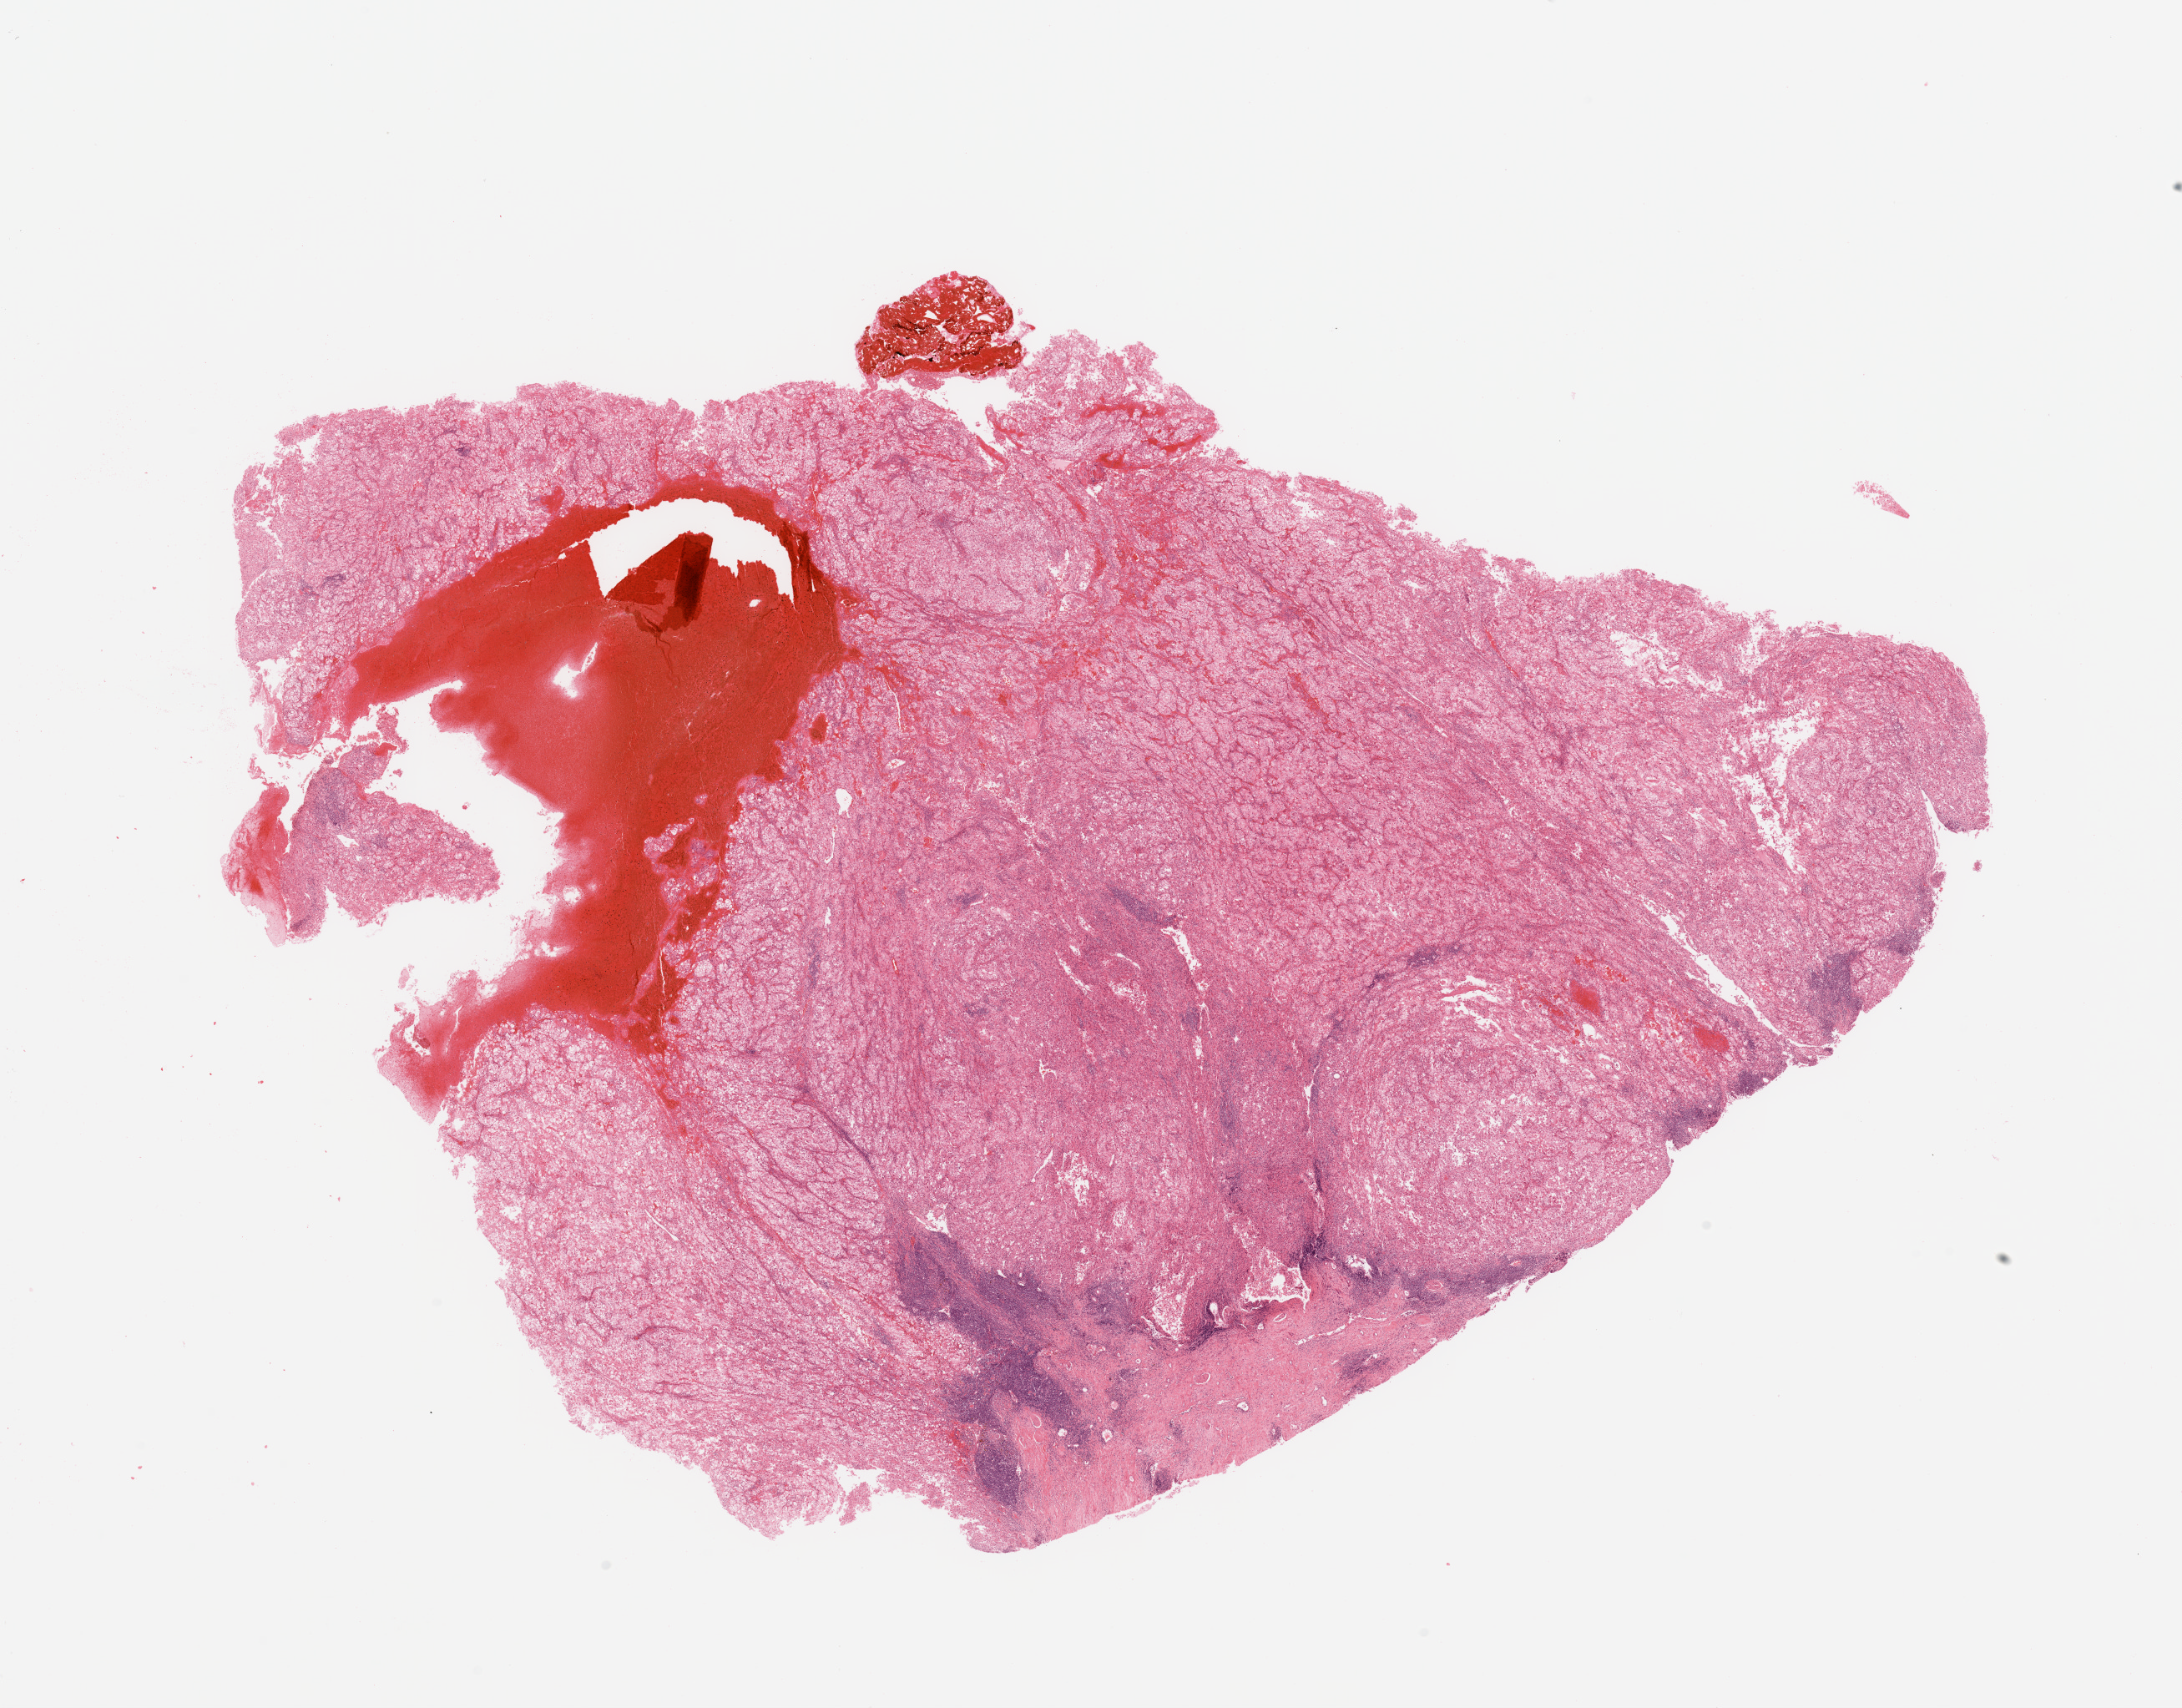
Whole-slide histology image, Hematoxylin and eosin (H&E) stained, low-resolution overview of the scanned area, about 20.7 x 16.2 mm (slide scanned at 20x); kidney, tumour tissue. 68-year-old male patient. Histologic grade: G3 (poorly differentiated).
- AJCC pathologic stage: II
- diagnosis: Renal cell carcinoma, NOS